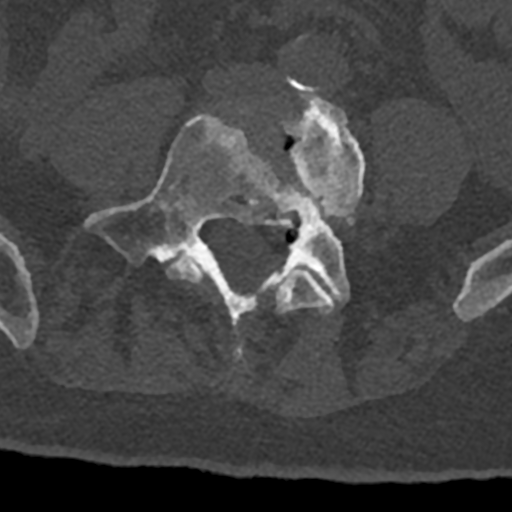
CT including the spine, one axial slice. Reconstruction kernel Br40s/3. 120 kVp. Bone window (W 1800 / L 400 HU). 0.5 mm slice thickness. 512 × 512 image matrix, field of view 160 × 160 mm. Male patient, age 74 years. Case-level facts recorded for this patient, not image findings: primary cancer: renal; vertebrae with lytic lesions (as recorded): T10, L1, L2, L3, L4, L5.
Outlined on this slice (semi-automatic segmentation, software-assisted and operator-edited):
- L4 vertebra: box from (x=166, y=91) to (x=365, y=370) px
- L5 vertebra: (x=83, y=115)–(x=350, y=354)